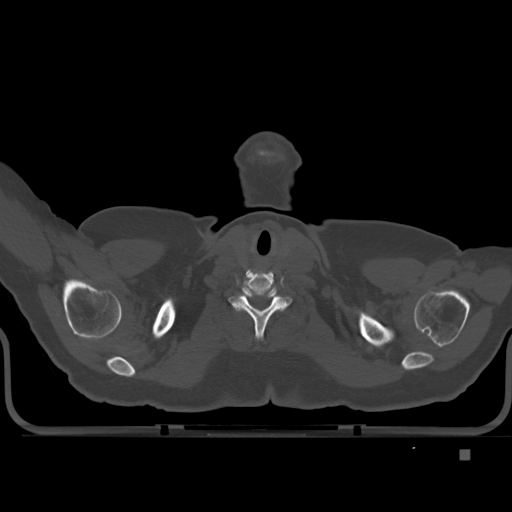
CT including the spine, one axial slice; position 413 of 477 along the scan axis; bone window (W 1800 / L 400 HU); 512 × 512 image matrix. Female patient, age 74 years. From the clinical record (not read from this slice): primary cancer: colon.
Annotated regions visible in this slice (semi-automatically segmented with operator editing):
- T1 vertebra: bounding box (x1, y1, x2, y2) in pixels: (266, 312, 275, 323)